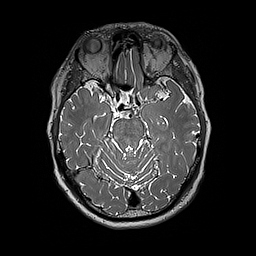
Brain MRI from a brain-tumour surgery series, one axial slice; slice 122 of 192 in the series (ordered by position); 1 mm slice thickness; 256 × 256 image matrix, field of view 250 × 250 mm. Case-level facts recorded for this patient, not image findings: histopathology: Glioblastoma; WHO grade: 4; IDH mutation: no.
Outlined on this slice (manually delineated by an expert):
- tumour: bounding box (x1, y1, x2, y2) in pixels: (144, 88, 148, 93)